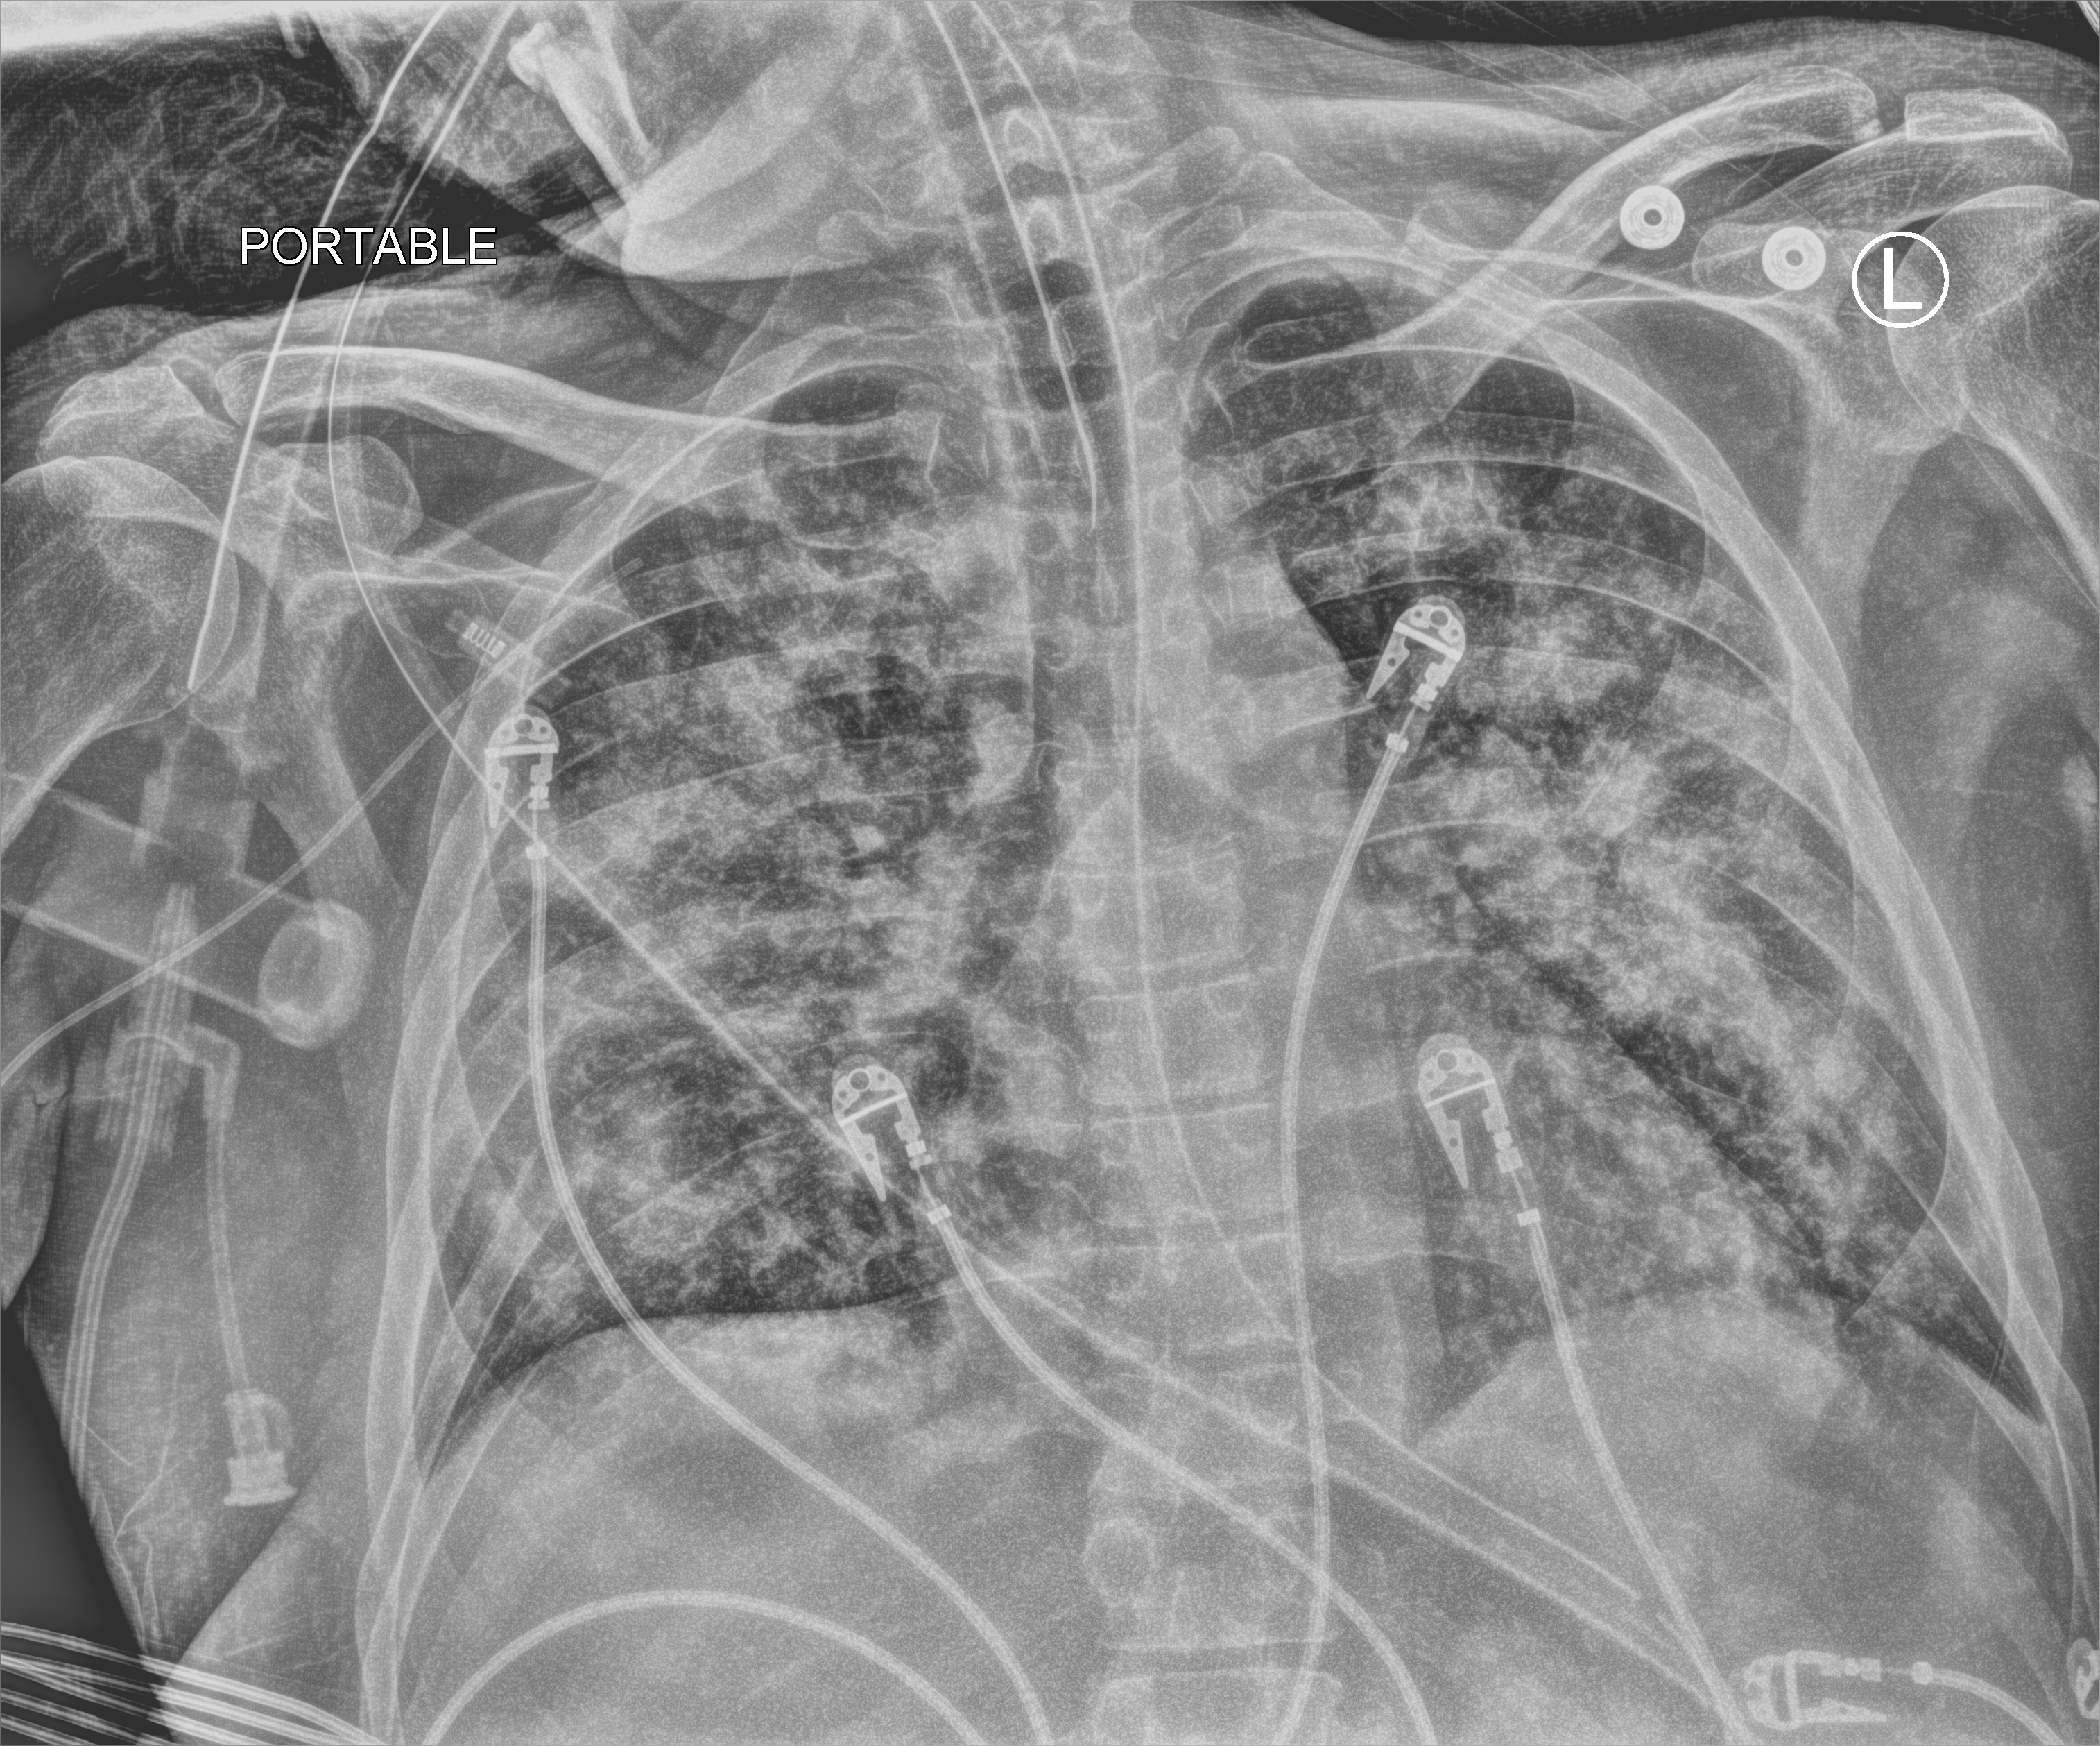
Portable chest radiograph; anteroposterior (AP) projection. Male patient hospitalised with COVID-19, age 18–59 years.
From the hospital-stay record, not from the radiograph (when in the stay this image was taken is not recorded): diabetes (admission record): yes; admitted to intensive care during this hospital stay: yes.